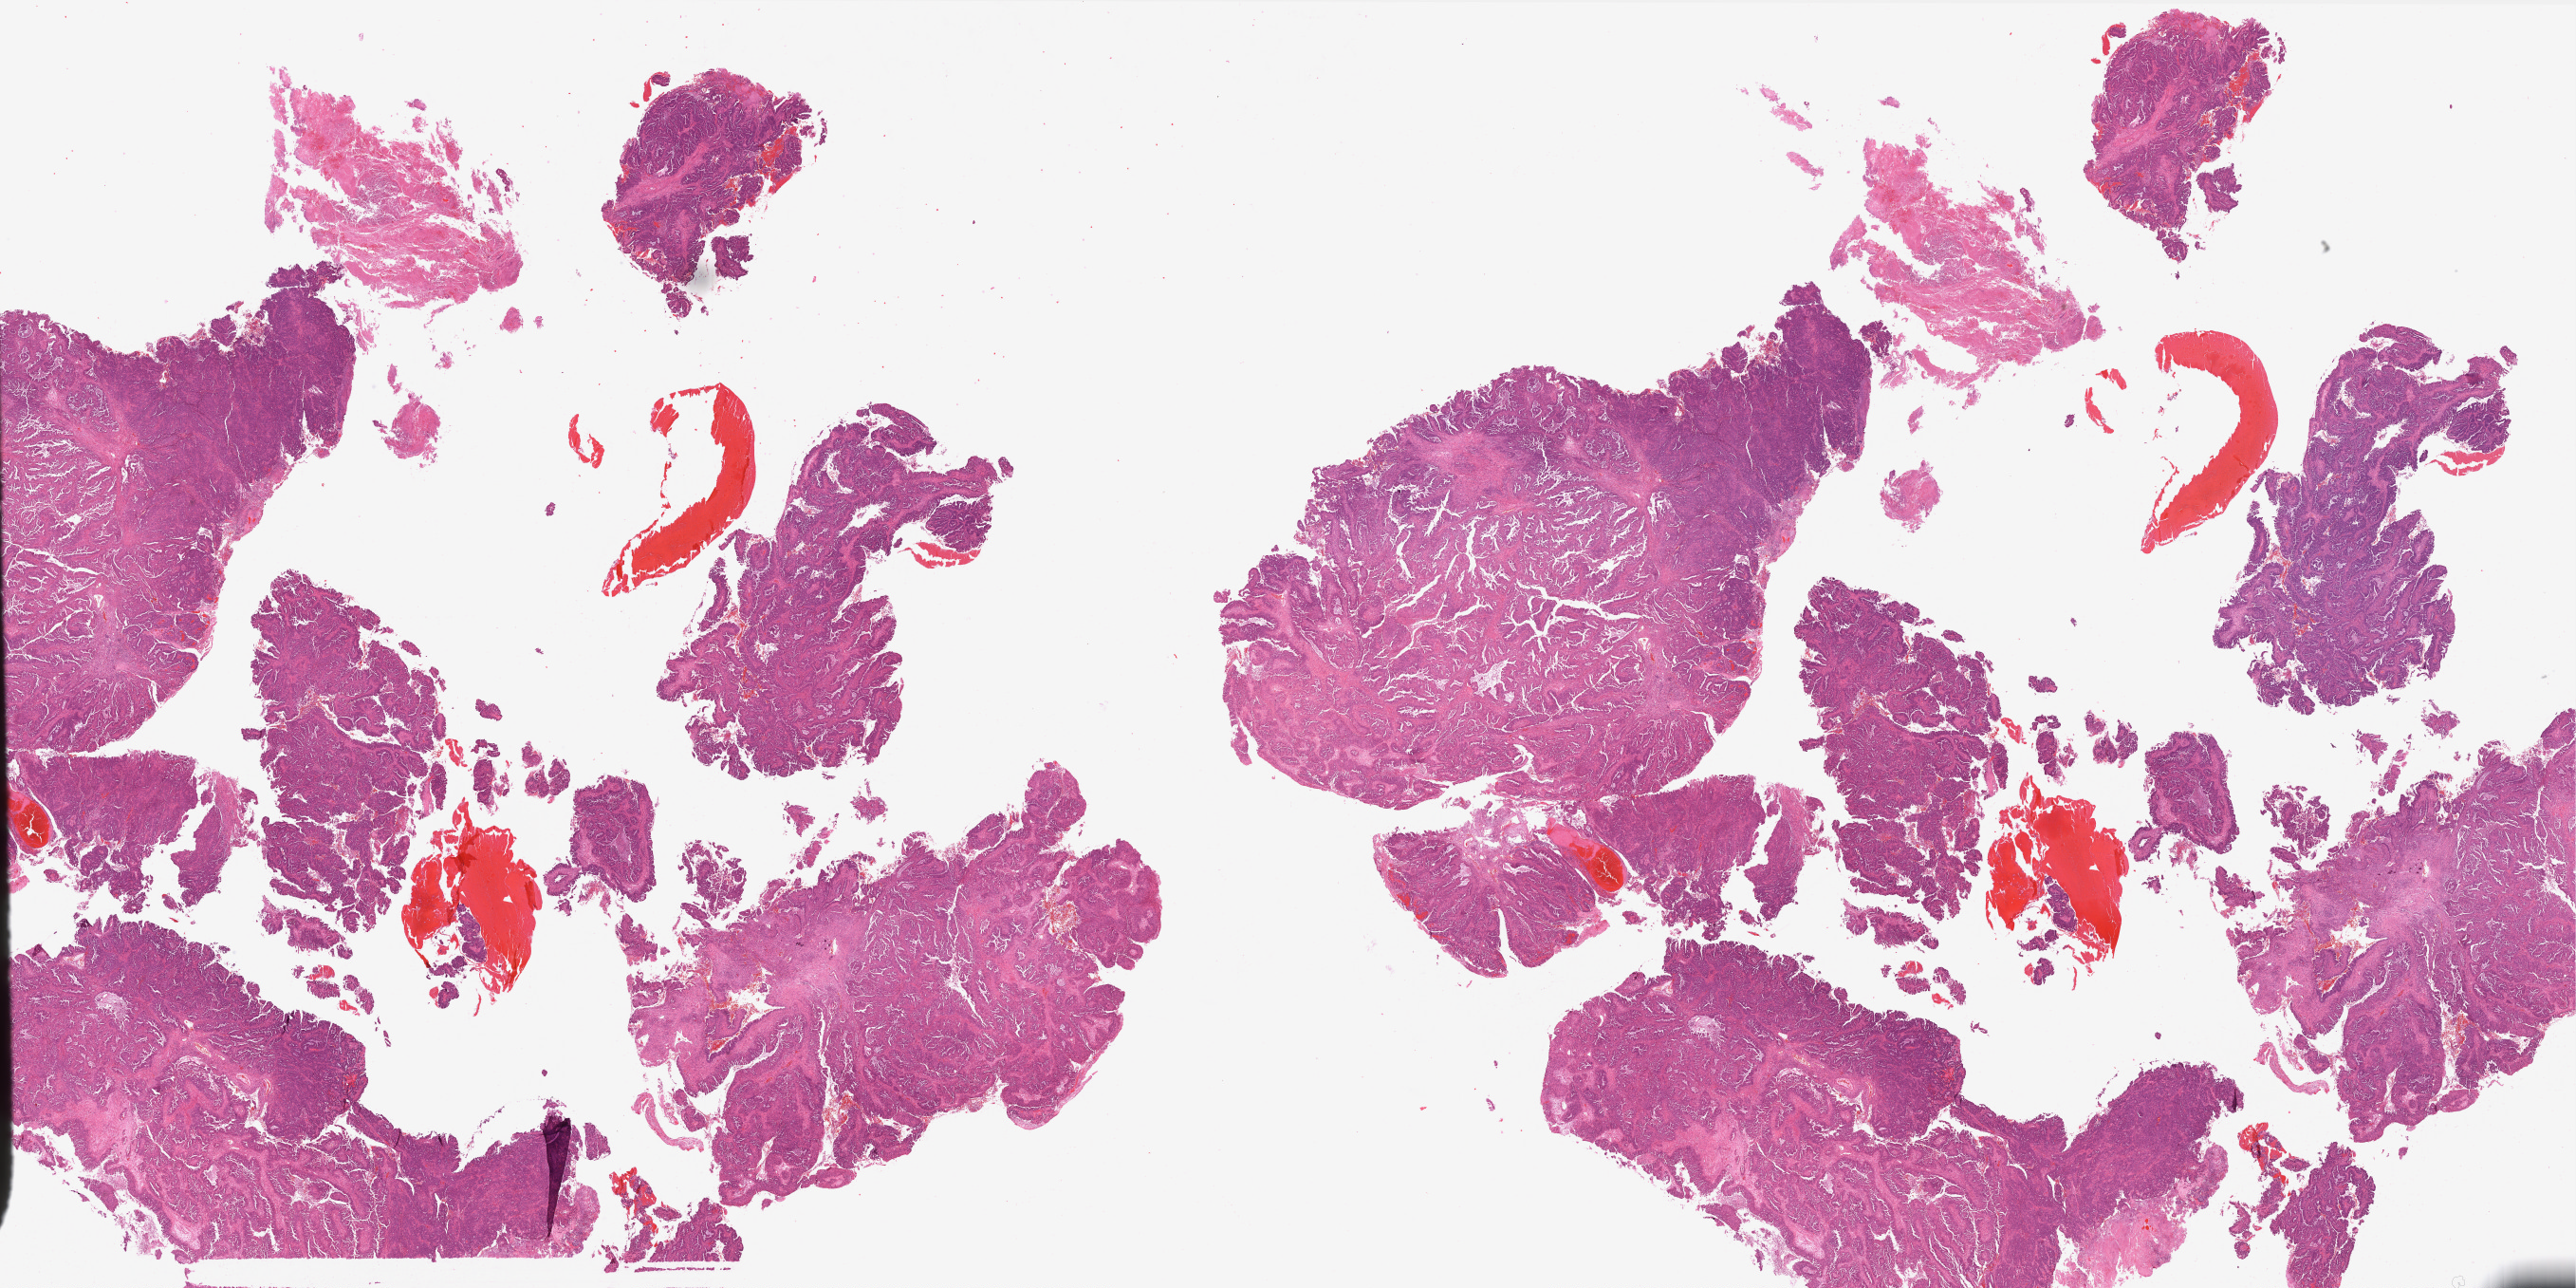
Digitized H&E tissue section (whole slide) — whole scanned area (about 43.5 x 21.7 mm, slide scanned at 40x) shown as a low-resolution overview; formalin-fixed paraffin-embedded (FFPE) diagnostic section; sample: primary tumour, cervix. Female patient; age at initial diagnosis 46 years. Histologic grade: G3 (poorly differentiated).
FIGO stage: IB1. Diagnosis: Adenocarcinoma, NOS (cervix uteri).